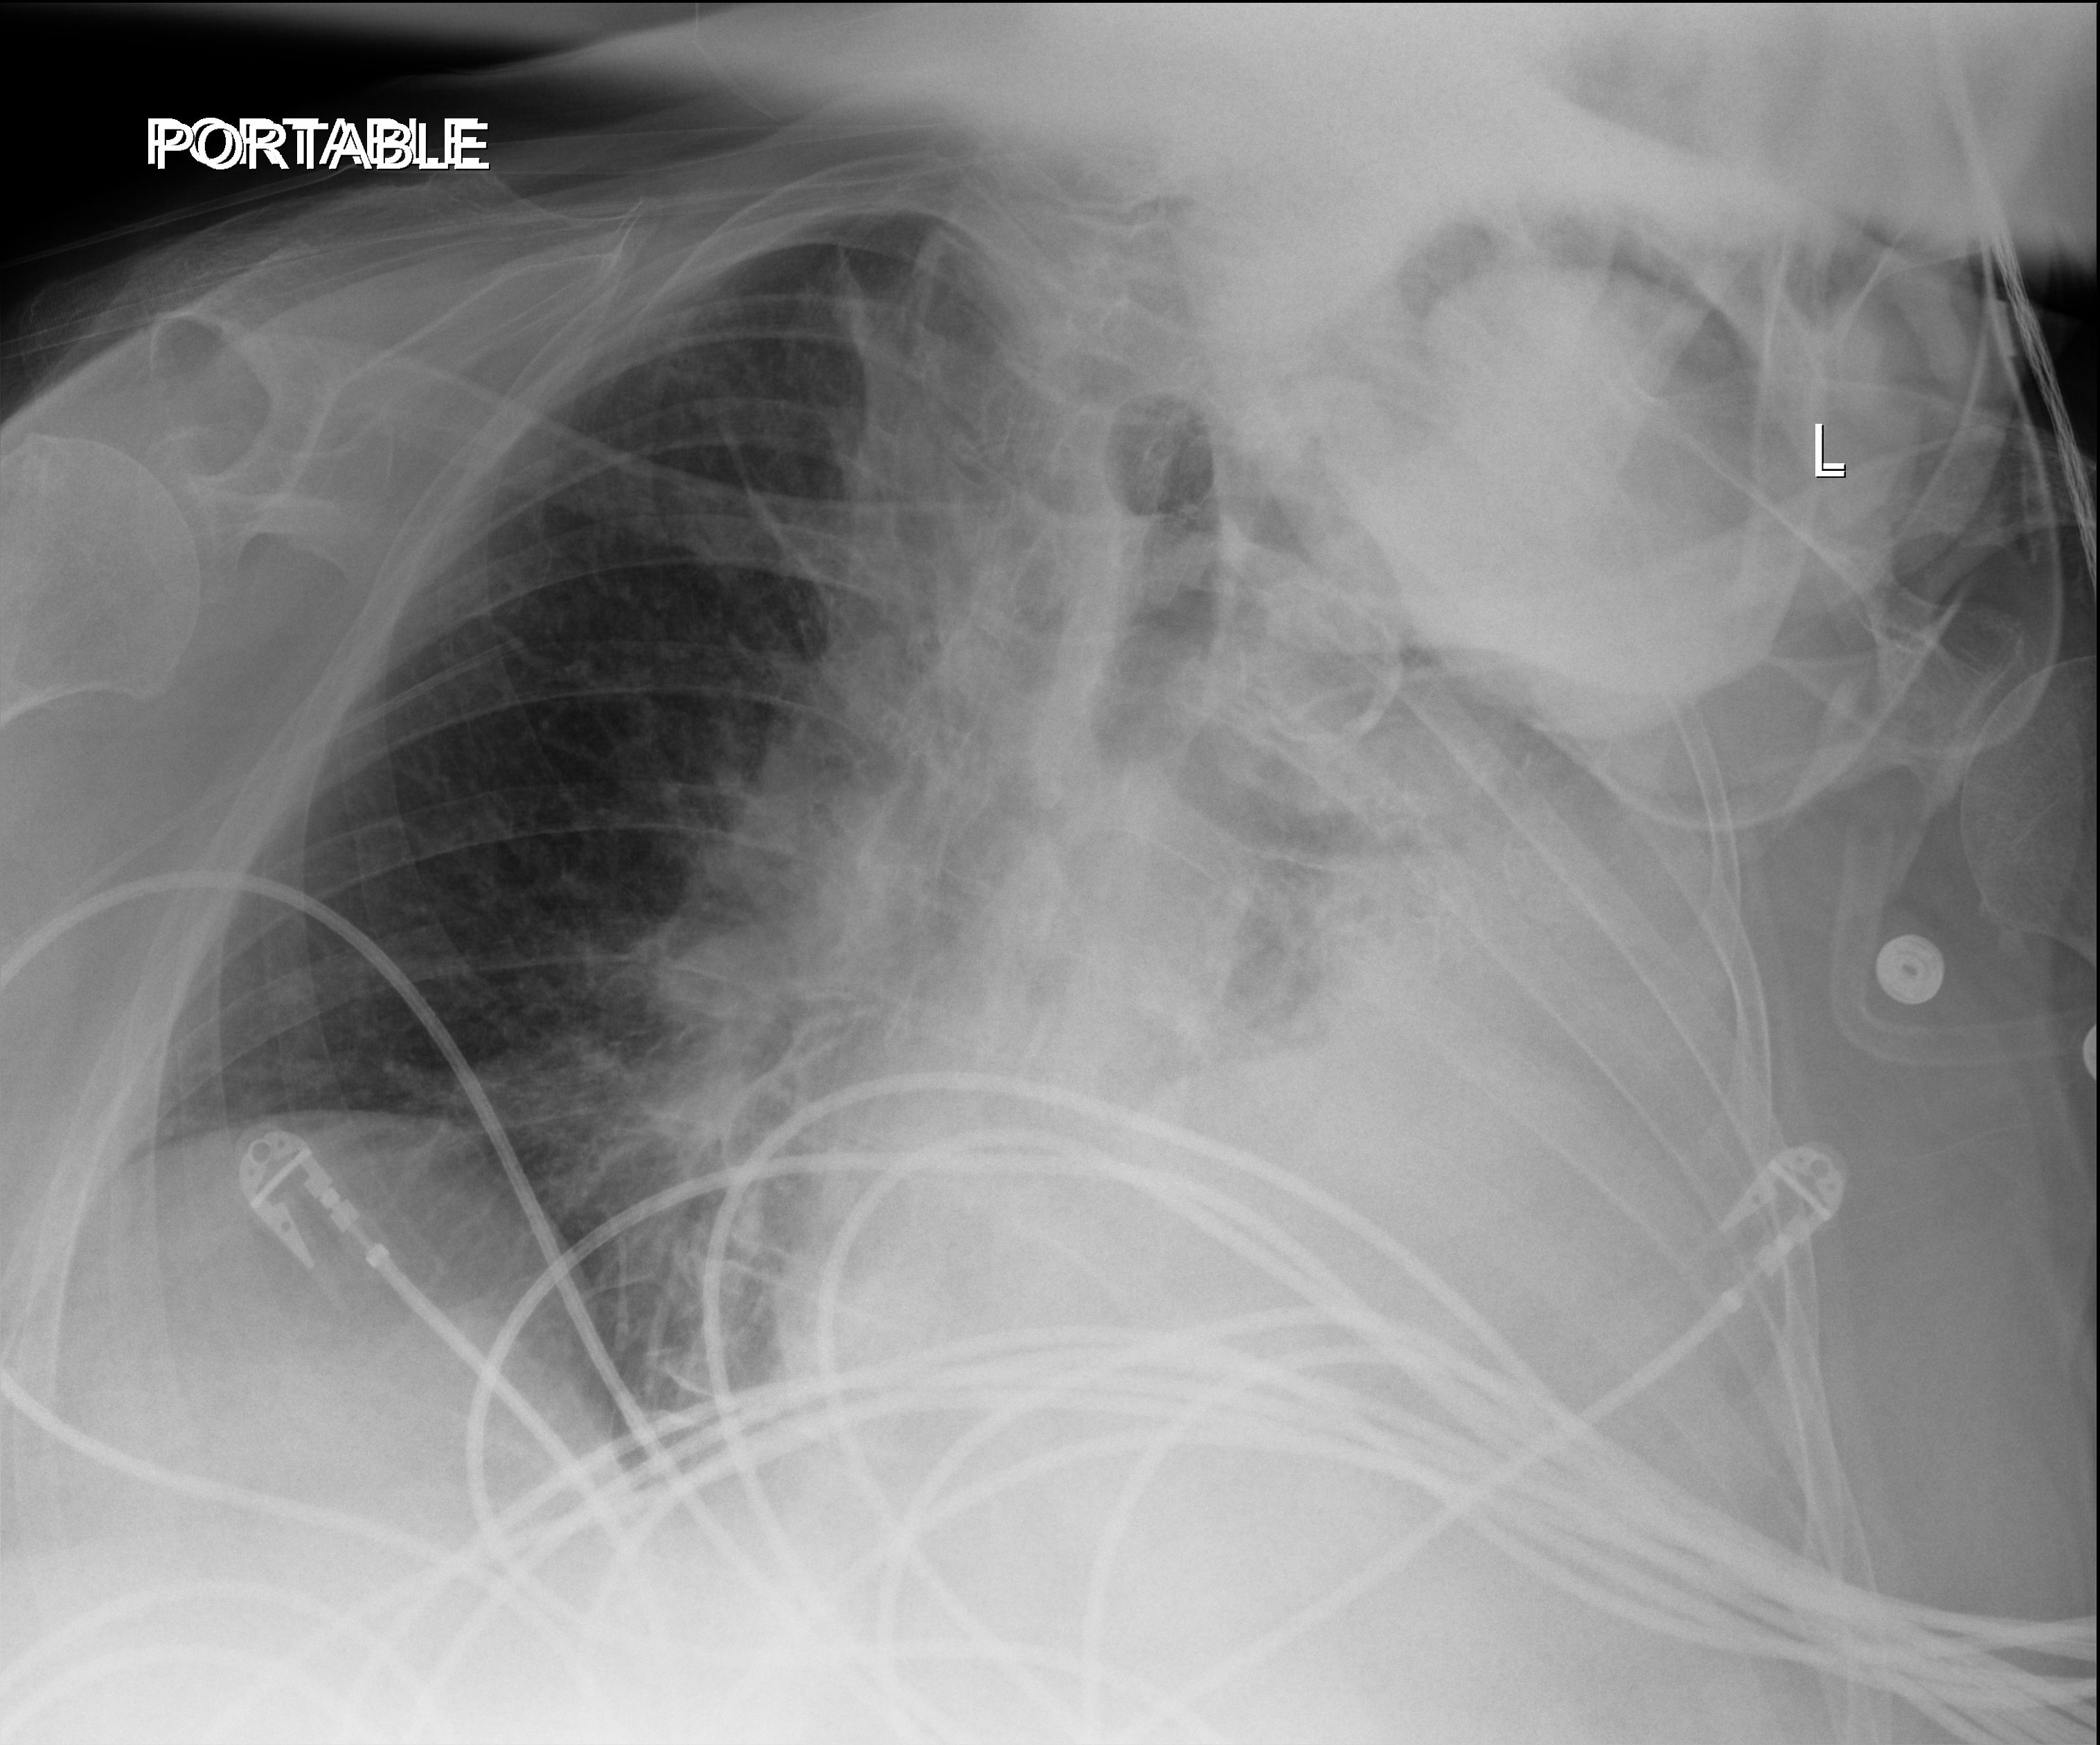
Bedside chest radiograph (digital radiography), anteroposterior (AP) projection. Patient hospitalised with COVID-19; female, aged 75–90 years.
From the hospital-stay record, not from the radiograph (when in the stay this image was taken is not recorded):
- mechanically ventilated during this hospital stay: no
- admitted to intensive care during this hospital stay: yes